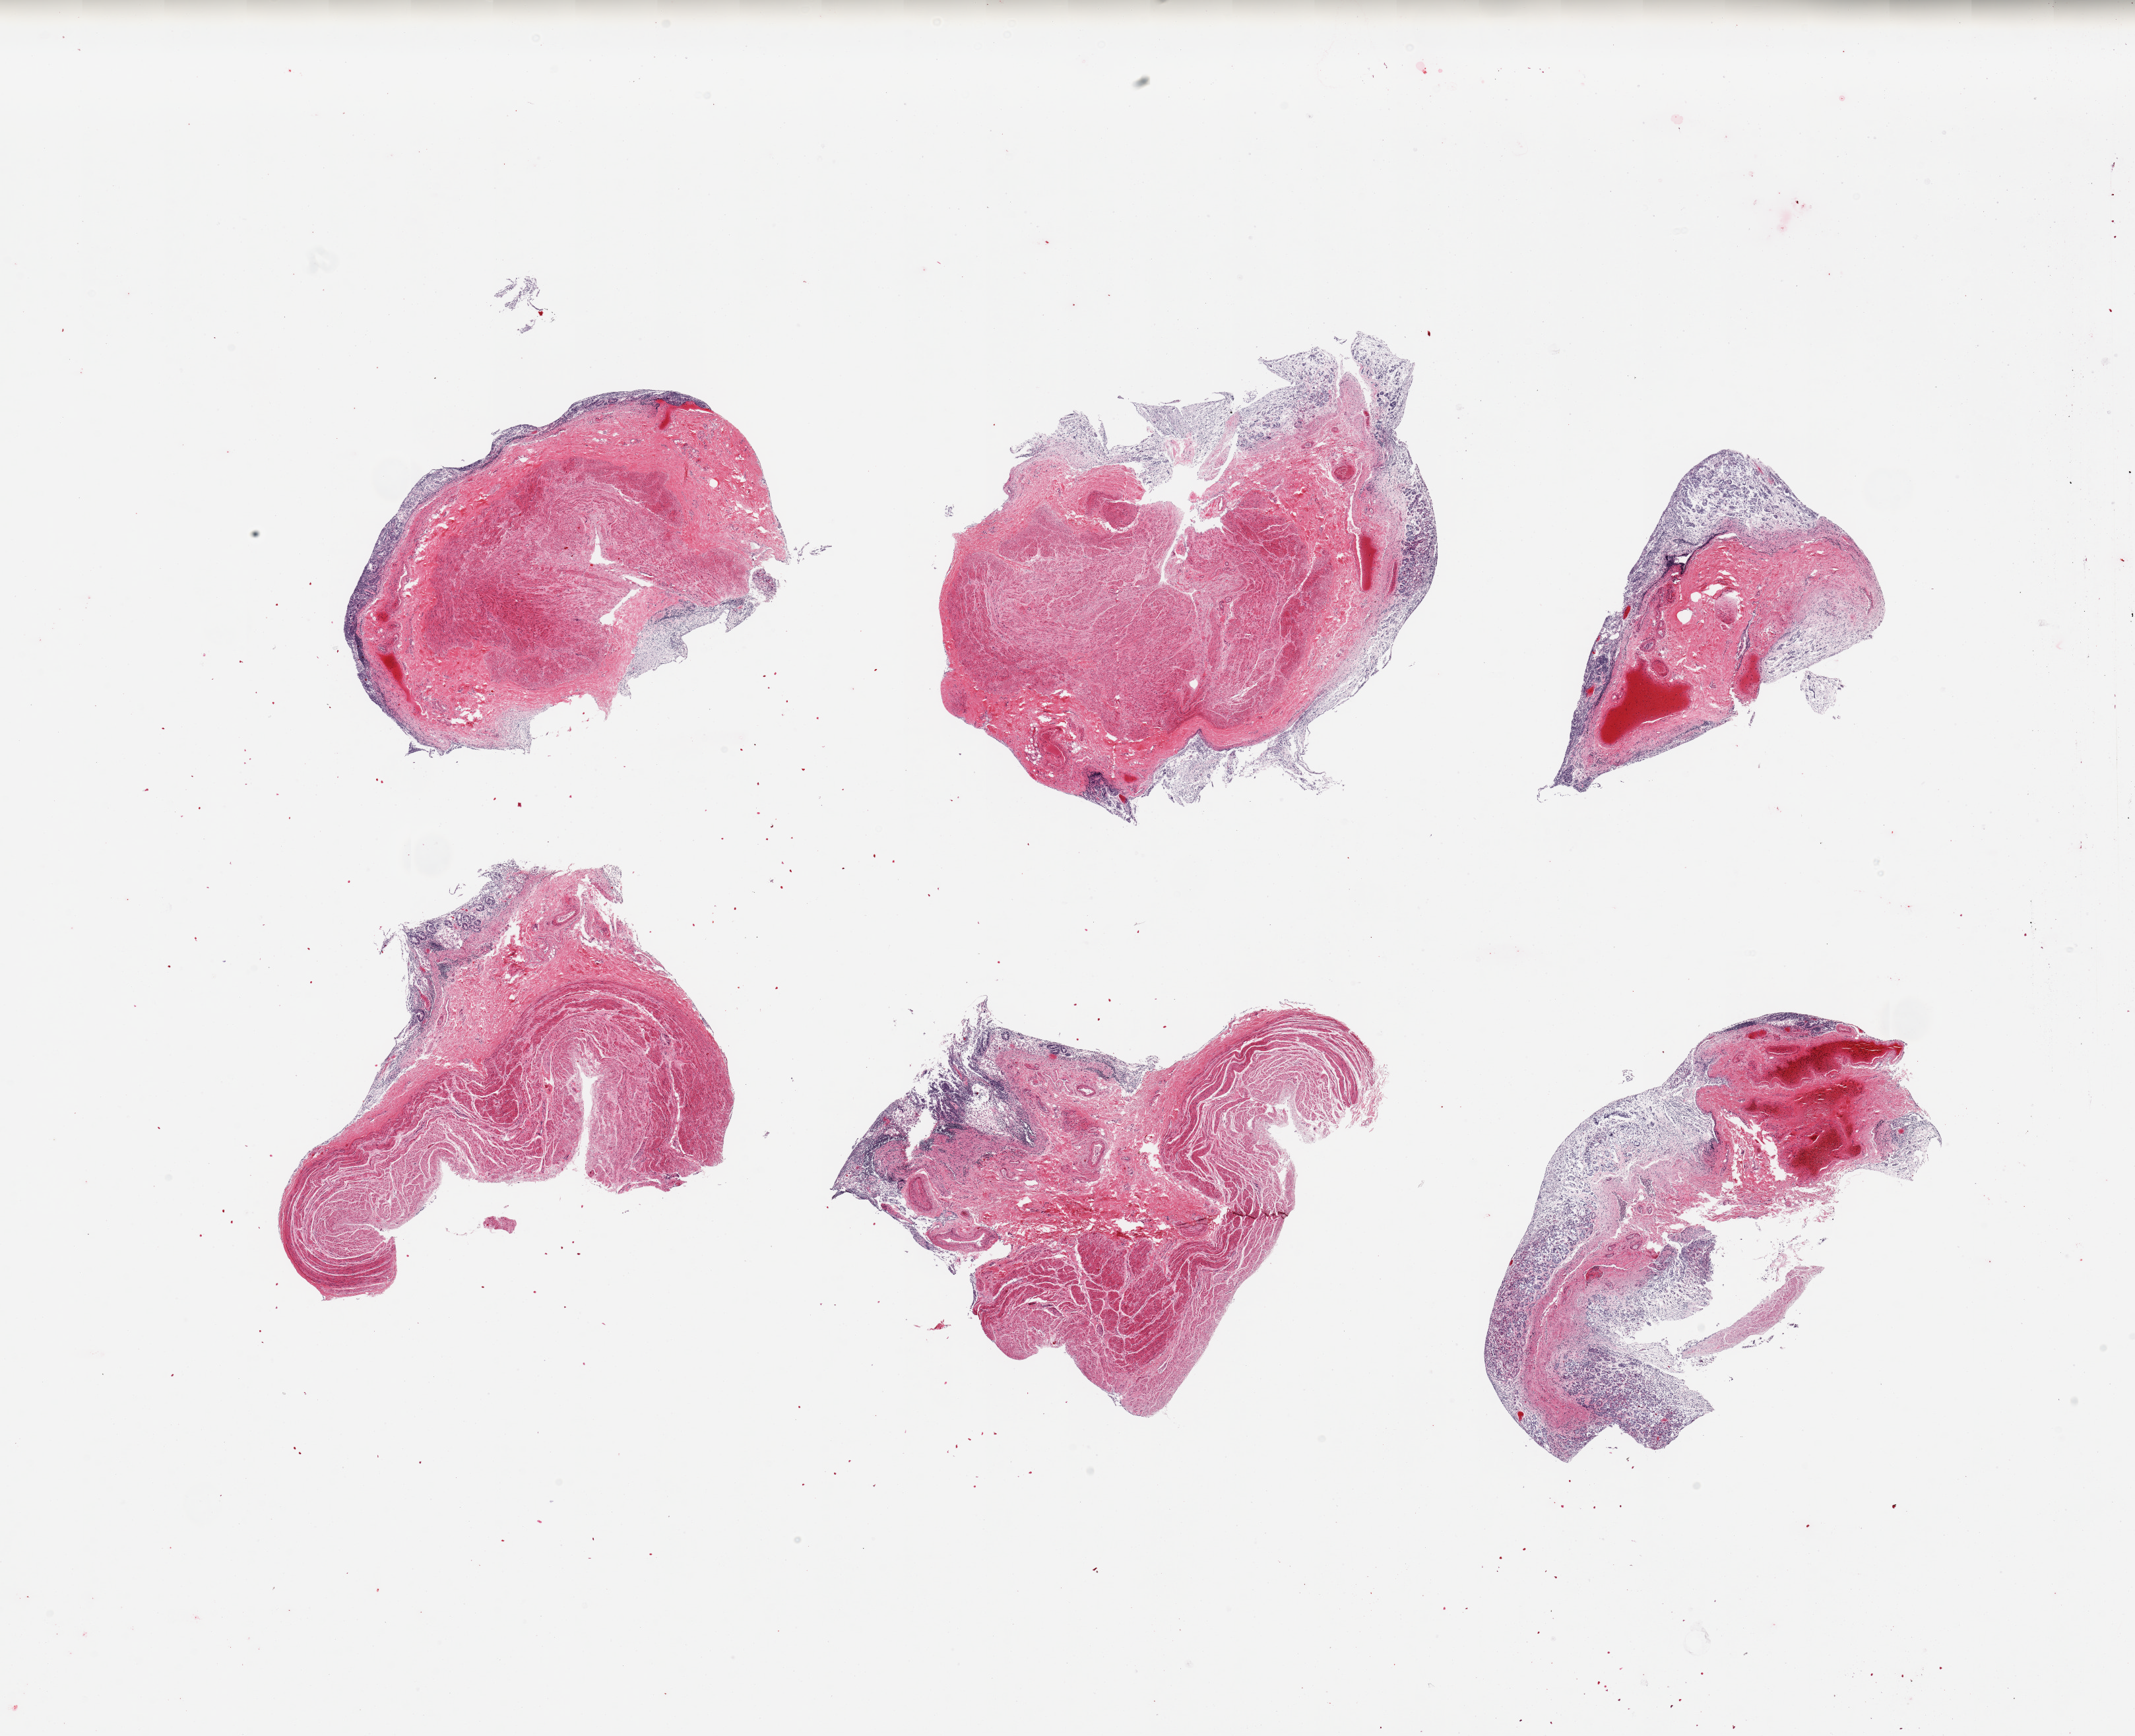
Haematoxylin and eosin whole-slide image, low-resolution overview of the scanned area, about 25.6 x 20.8 mm, PAXgene-fixed paraffin-embedded (PFPE) section, target tissue: stomach, donor tissue sample. Donor: male.
- review note (as recorded): 6 pieces; mucosa autolyzed, muscle intact